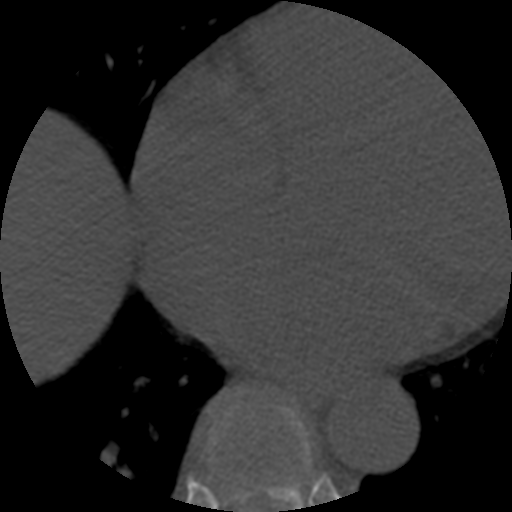
CT including the spine, one axial slice. Position 321 of 508 along the scan axis. Reconstruction kernel STANDARD. 120 kVp. Bone window (W 1800 / L 400 HU). 1.25 mm slice thickness. 512 × 512 image matrix, field of view 160 × 160 mm. Patient age 57 years. Case-level facts recorded for this patient, not image findings: primary cancer: prostate.
Structures marked on this image (semi-automatic segmentation, software-assisted and operator-edited):
- T7 vertebra: bounding box <209,405,249,512> (left, top, right, bottom; pixels)
- T8 vertebra: <213,392,313,512>